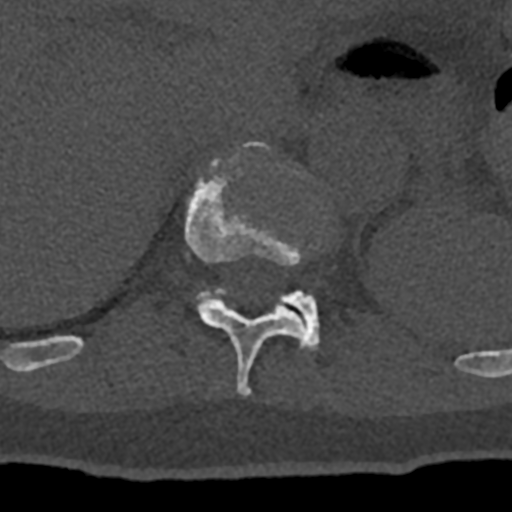
CT including the spine, one axial slice. Slice 532 of 797 in the series (ordered by position). Reconstruction kernel Br40s/3. 120 kVp. Bone window (W 1800 / L 400 HU). 512 × 512 image matrix. Patient: male, 74 years. From the clinical record (not read from this slice): primary cancer: renal; vertebrae with lytic lesions (as recorded): T10, L1, L2, L3, L4, L5.
Outlined on this slice (semi-automatic segmentation, software-assisted and operator-edited):
- T11 vertebra: bounding box <70,141,308,397> (left, top, right, bottom; pixels)
- T12 vertebra: <198,289,320,351>